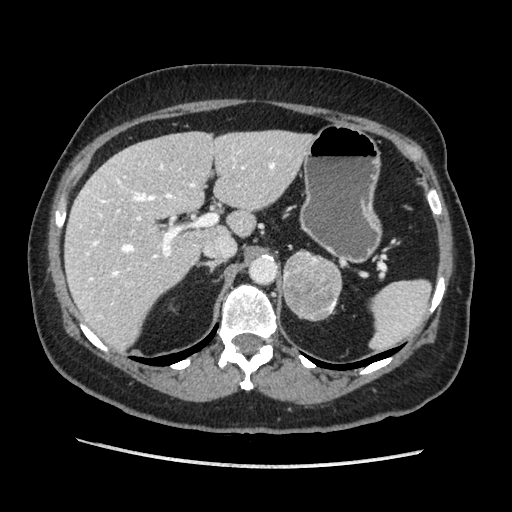
Contrast-enhanced abdominal CT, one axial slice; position 129 of 203 along the scan axis; soft-tissue window (W 400 / L 40 HU); 1.25 mm slice thickness; 512 × 512 image matrix, field of view 360 × 360 mm. Female patient. From the clinical record (not read from this slice): diagnosis: adrenocortical carcinoma; tumour side: left adrenal; tumour size at pathology: 6.5 cm; Ki-67 index: 22 %; stage (as recorded): 2.
Annotated regions visible in this slice (semi-automatically segmented with operator editing):
- mass: bounding box [x1, y1, x2, y2] px = [283, 250, 343, 320]